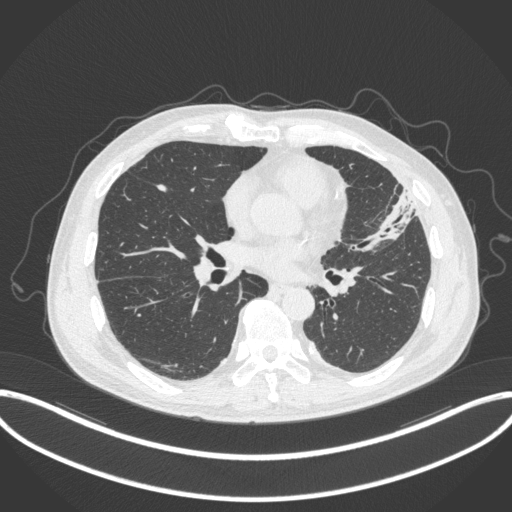
Chest CT, one axial slice; position 156 of 382 along the scan axis; 120 kVp; lung window (W 1500 / L -600 HU); 1 mm slice thickness; 512 × 512 image matrix. Male patient, age 64 years. From the clinical record (not read from this slice): clinical TNM (as recorded): T4 N1 M0.
Structures marked on this image (rectangle marked by the reading radiologist):
- lung tumour (recorded histology: adenocarcinoma): box from (x=365, y=188) to (x=422, y=253) px